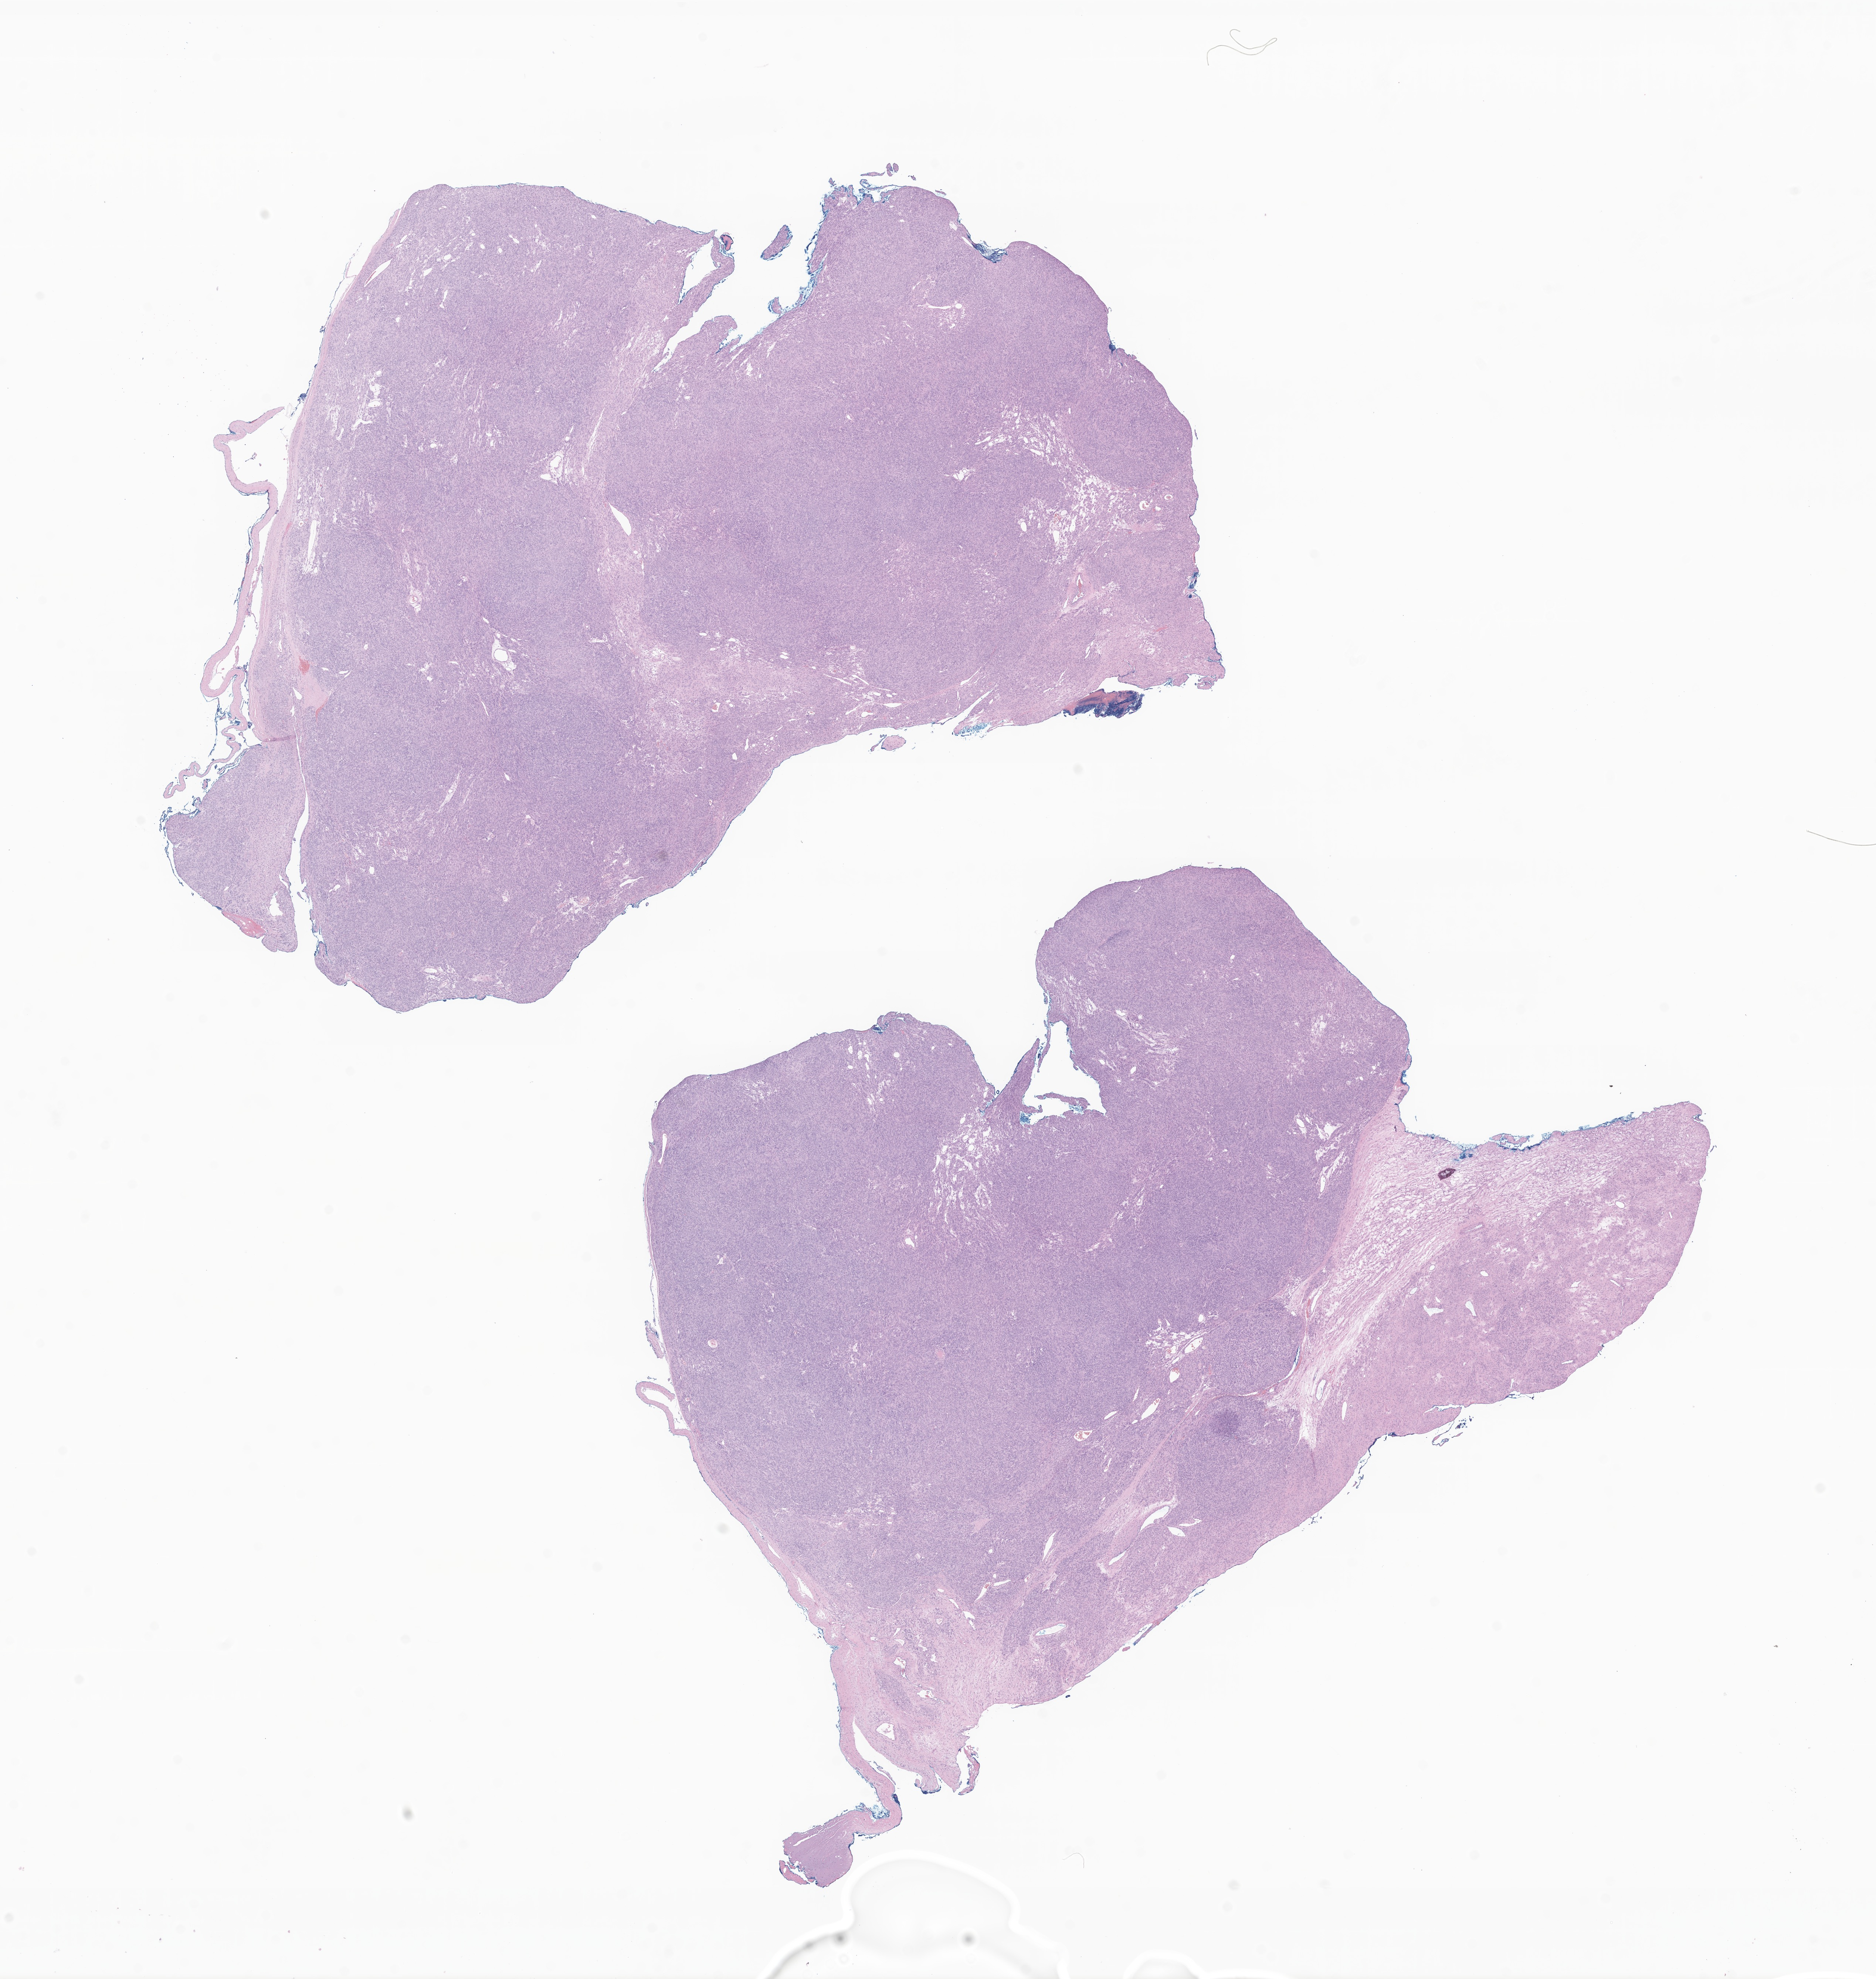
Digitized H&E-stained section of tumor tissue from the lower limb — a low-resolution overview of the entire scanned area, about 21.4 x 22.6 mm. Formalin-fixed paraffin-embedded section. Patient: female, age 222 months (18 years 6 months).
Diagnosis (ICD-O-3 morphology term): Leiomyosarcoma, NOS.